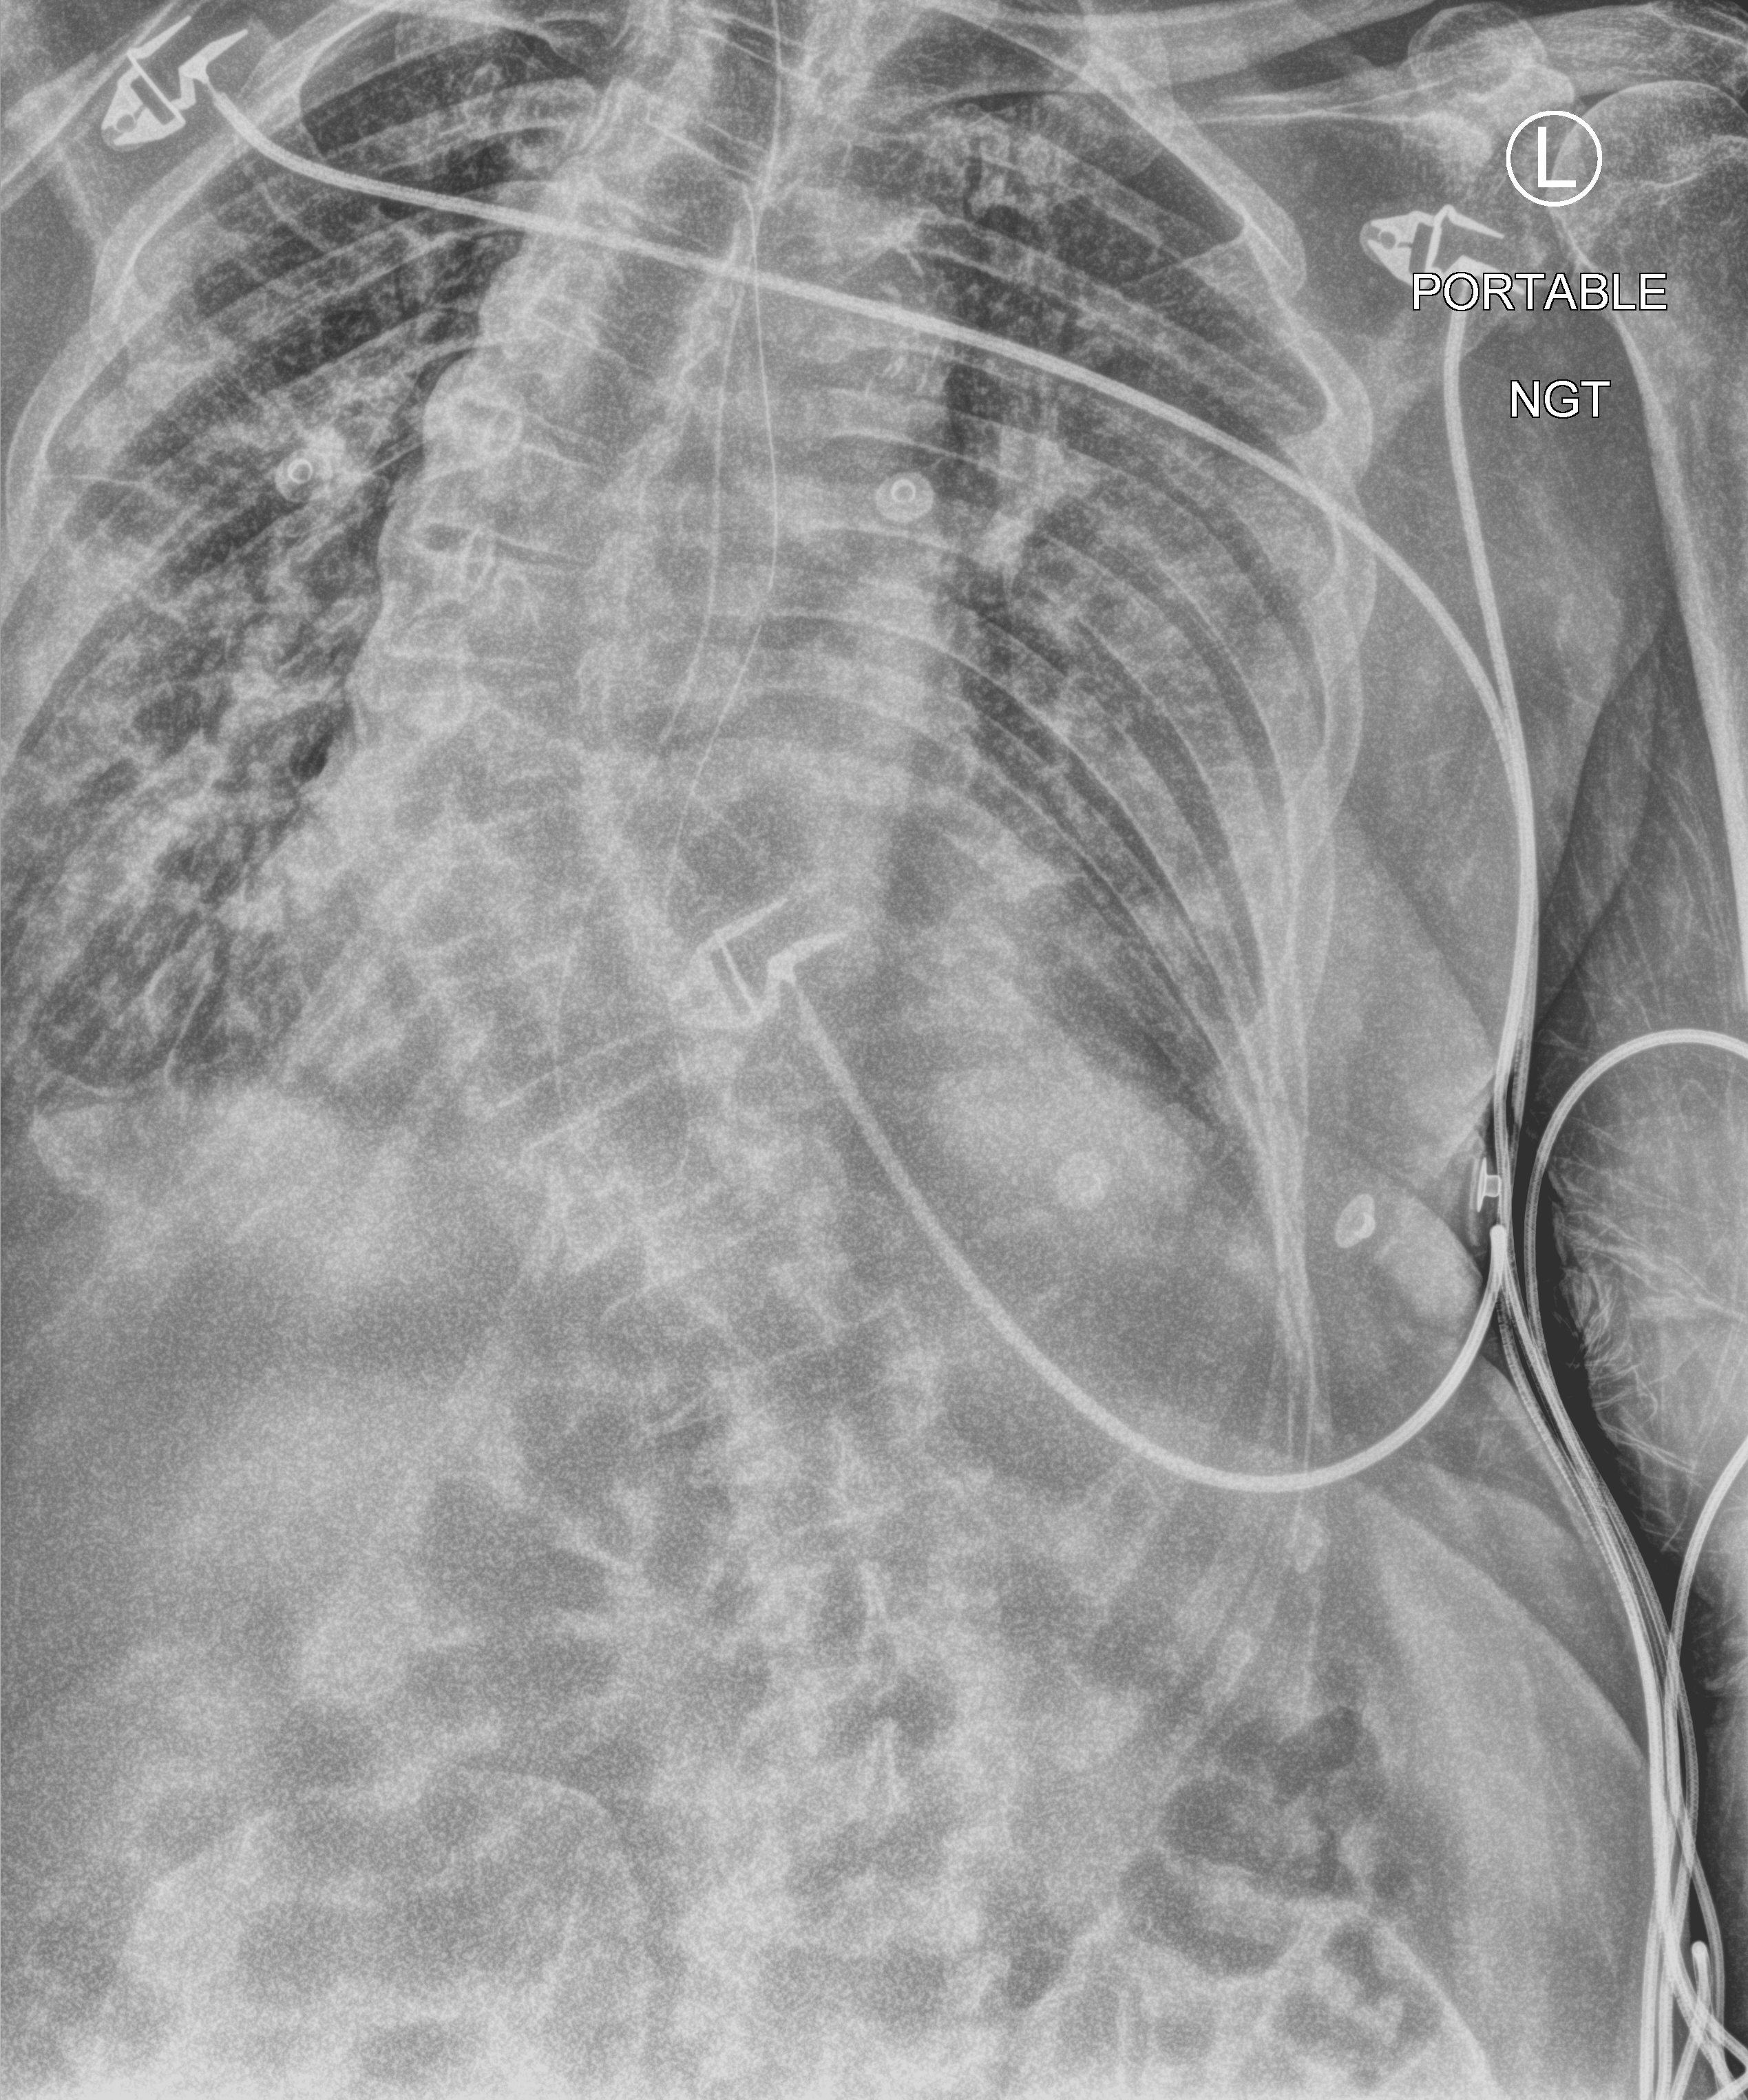
Bedside chest radiograph (computed radiography), anteroposterior (AP) projection. Male patient hospitalised with COVID-19, age 75–90 years.
Hospital-stay facts (about this admission, not read from this image; timing relative to this image not recorded): length of hospital stay: 12 days; admitted to intensive care during this hospital stay: no.